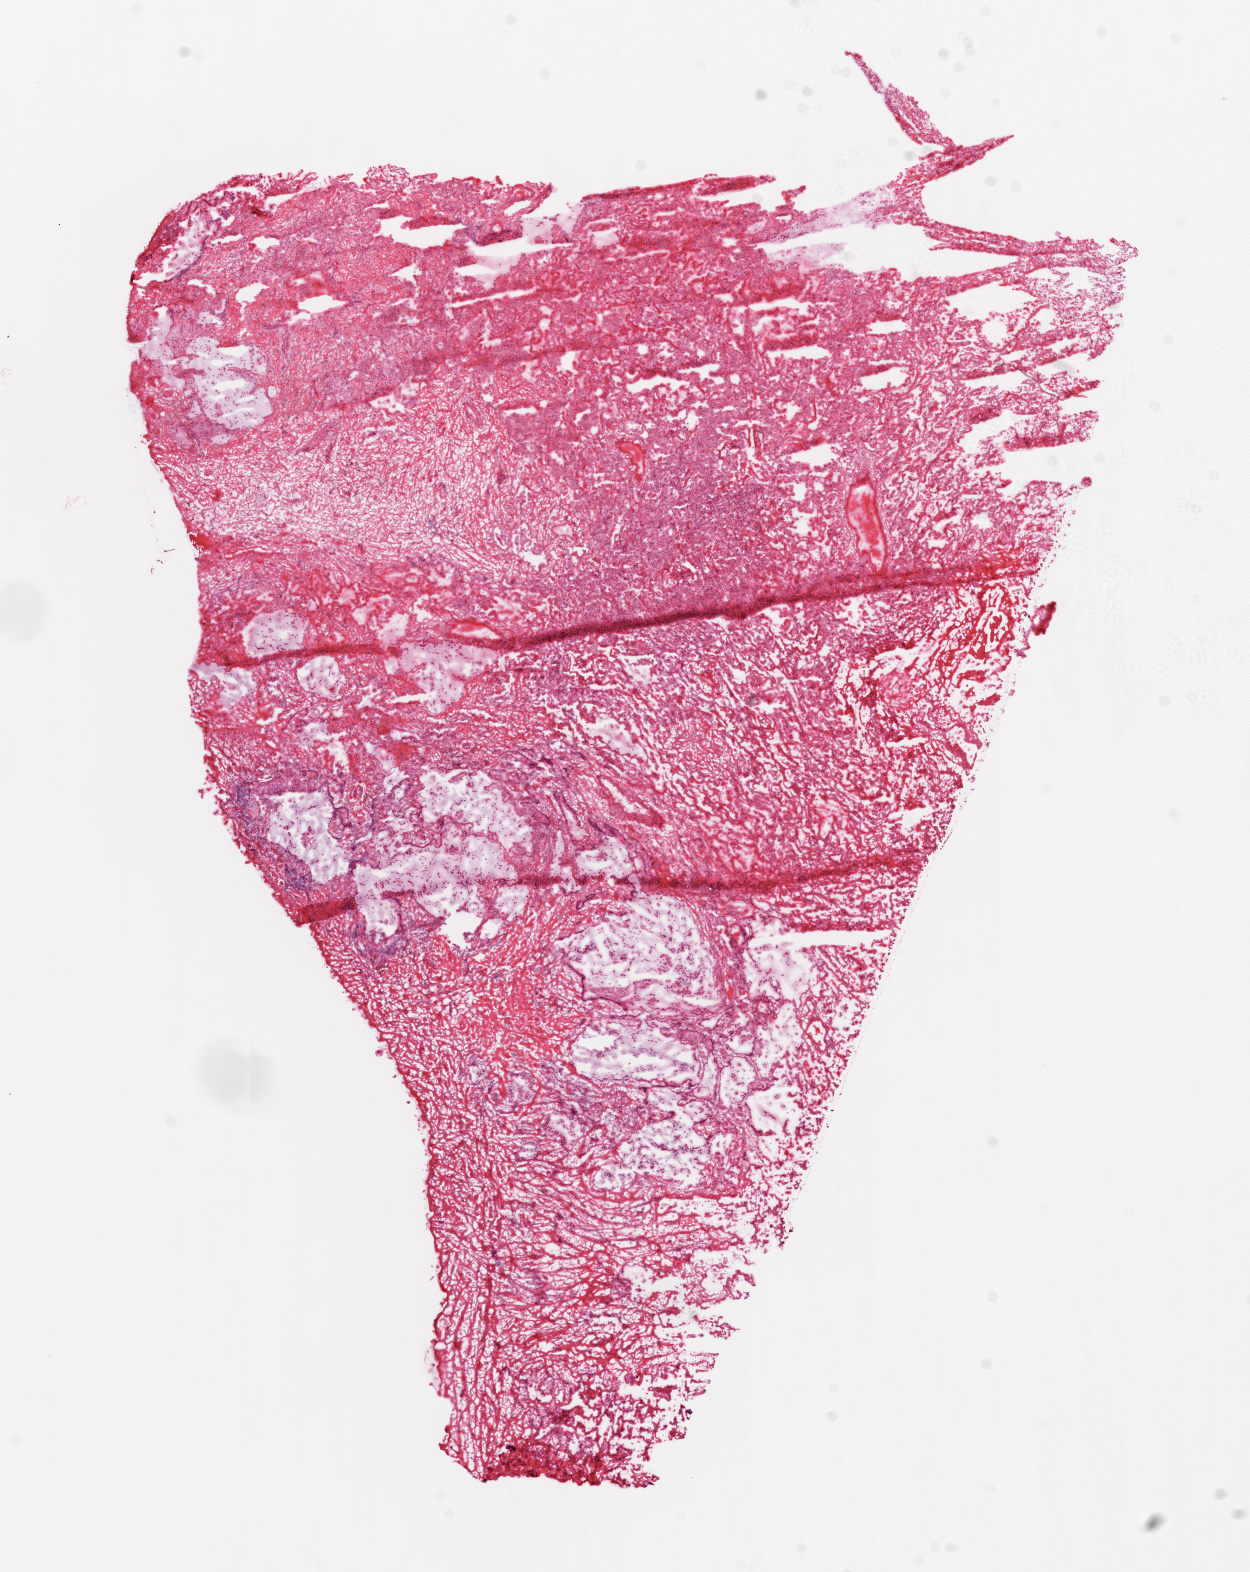
Whole-slide histology image, Hematoxylin and eosin (H&E) stained — a low-resolution overview of the entire scanned area, about 10.0 x 12.6 mm (slide scanned at 20x), frozen section from the top of the tissue portion, lung, solid tissue normal (non-tumour tissue) sample. Male, age 65 years at initial diagnosis.
- this section: solid tissue normal sample (biorepository sample class)
- patient diagnosis: Squamous cell carcinoma, NOS